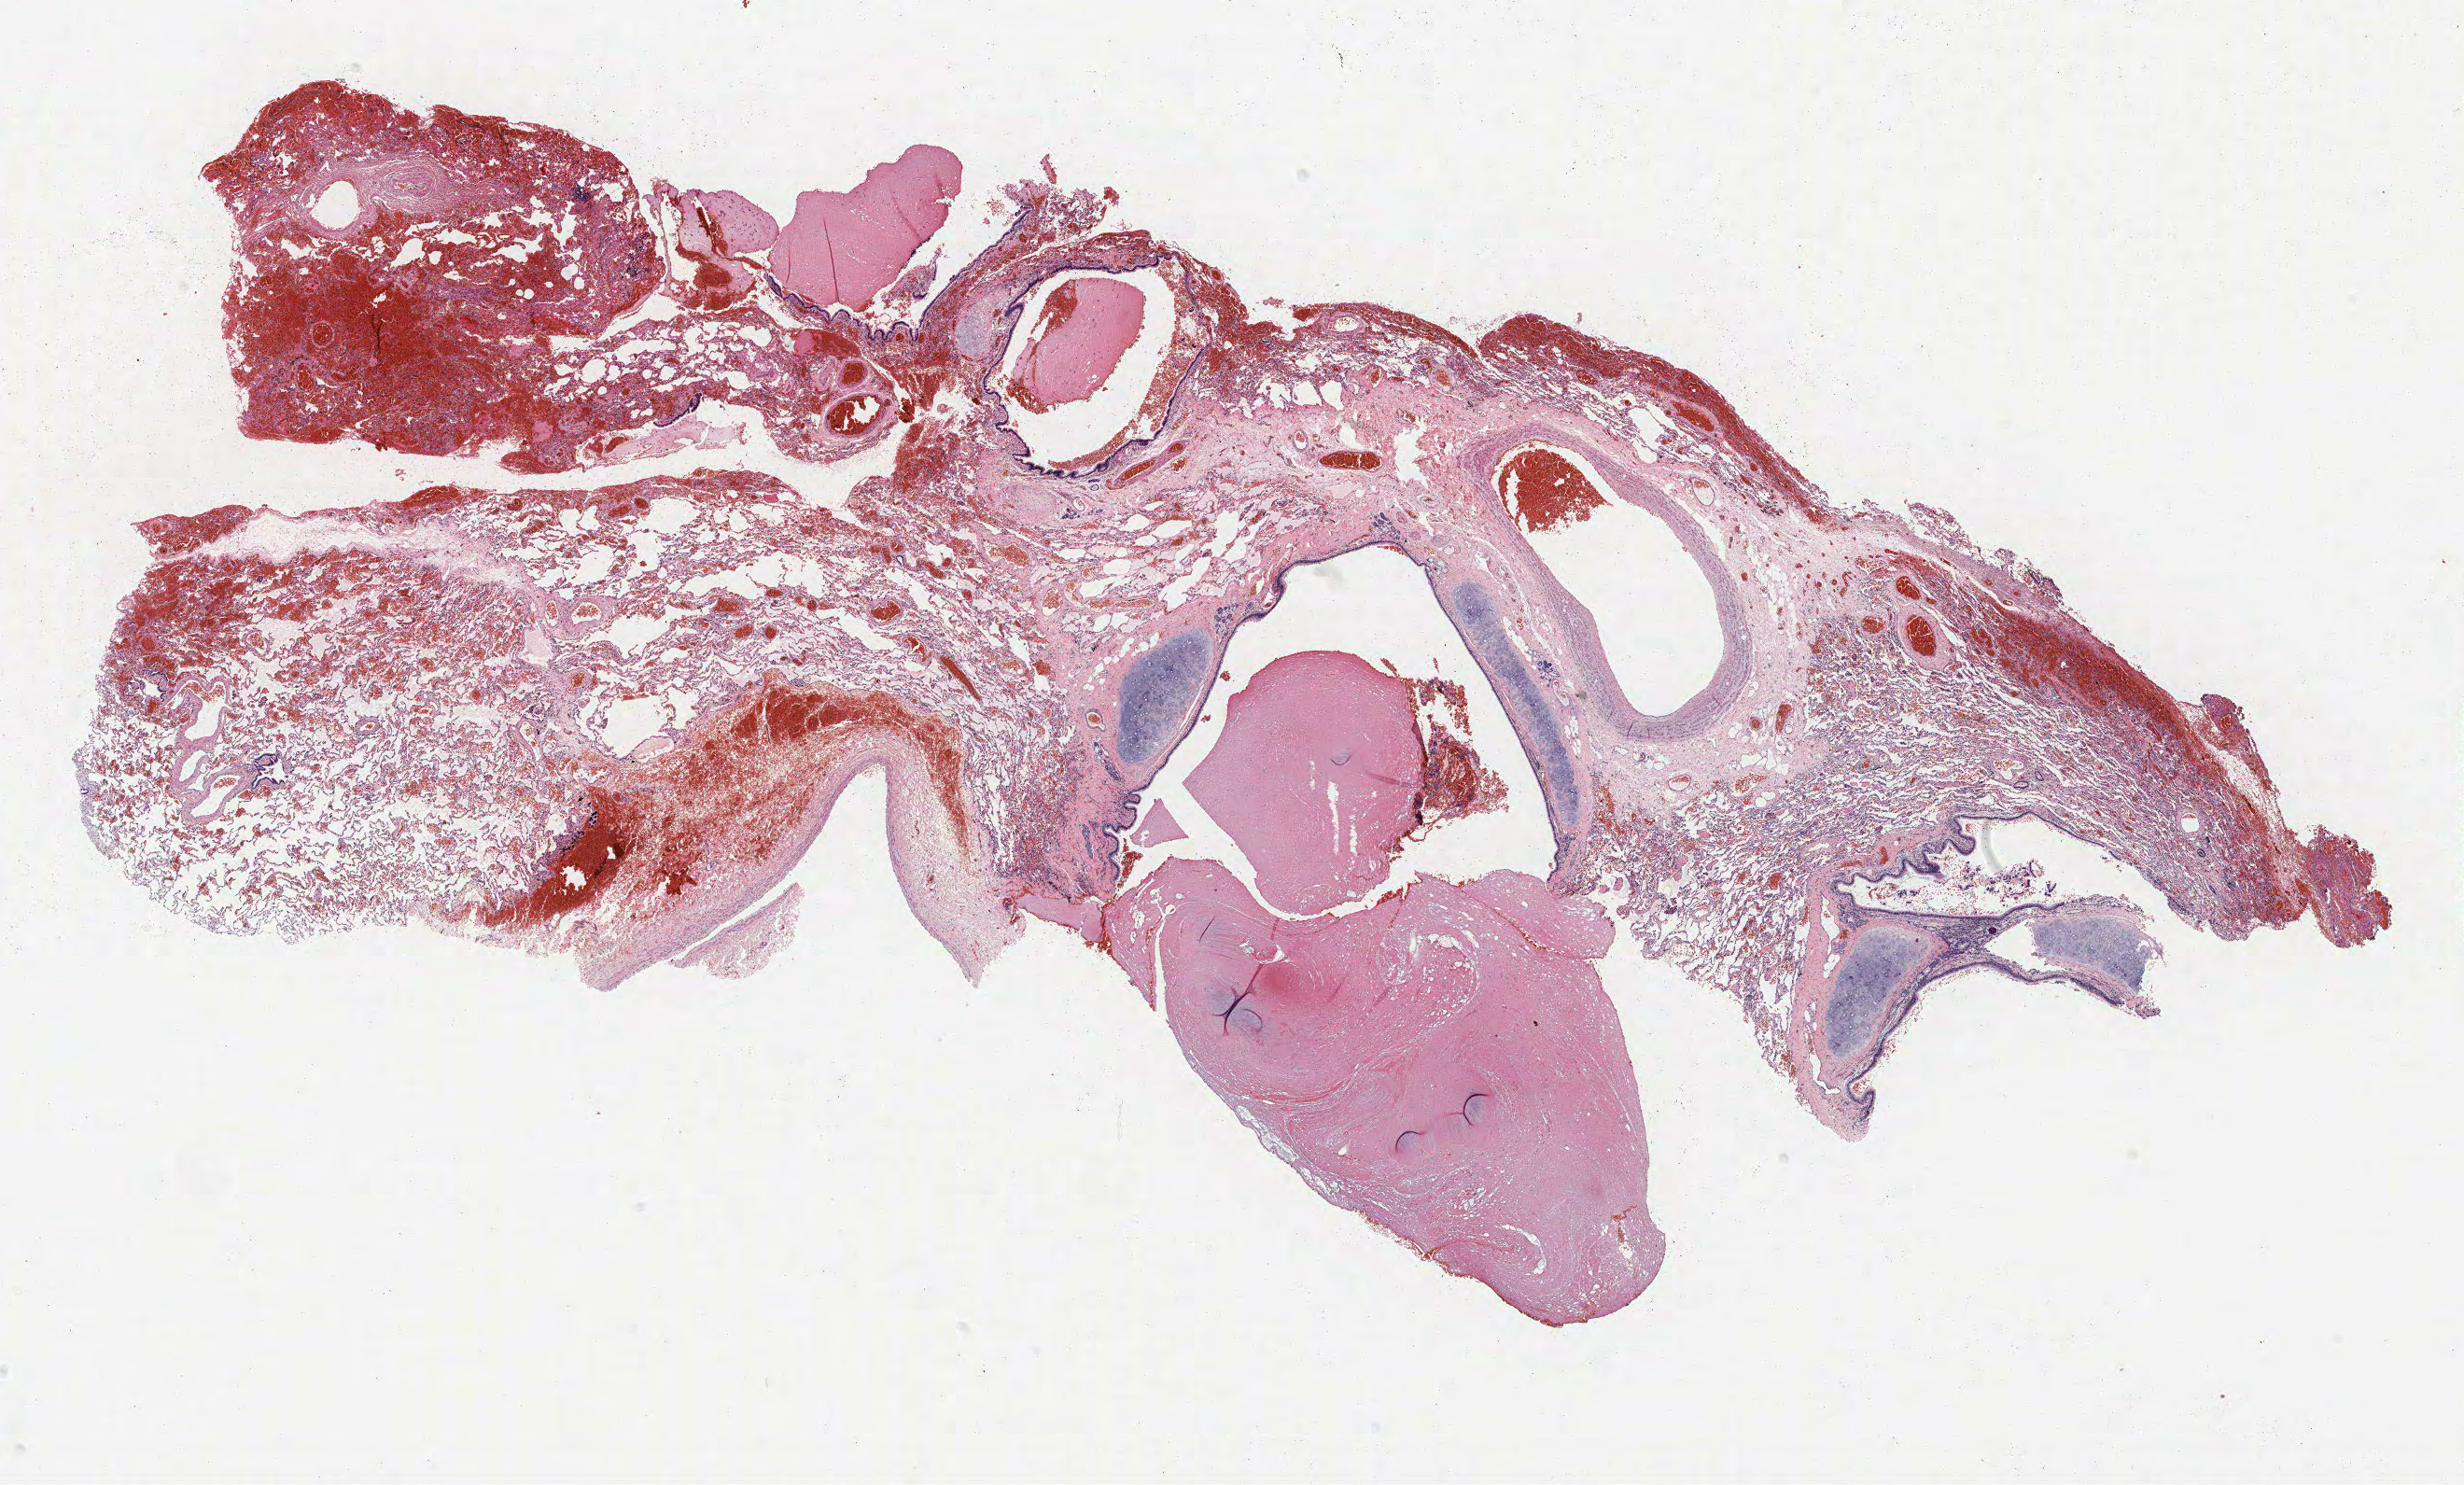
Hematoxylin and eosin (H&E) stained whole-slide image — low-resolution overview of the scanned area, about 21.1 x 12.7 mm (from a 40x scan); FFPE section; lung tissue. Male patient, aged 57 at enrolment.
- participant's lung-cancer diagnosis: Carcinoid tumor, NOS (ICD-O-3 8240/3)
- primary tumour location (clinical record): right middle lobe
- stage (AJCC 7th edition): IA
- tumour size (pathology): 15 mm